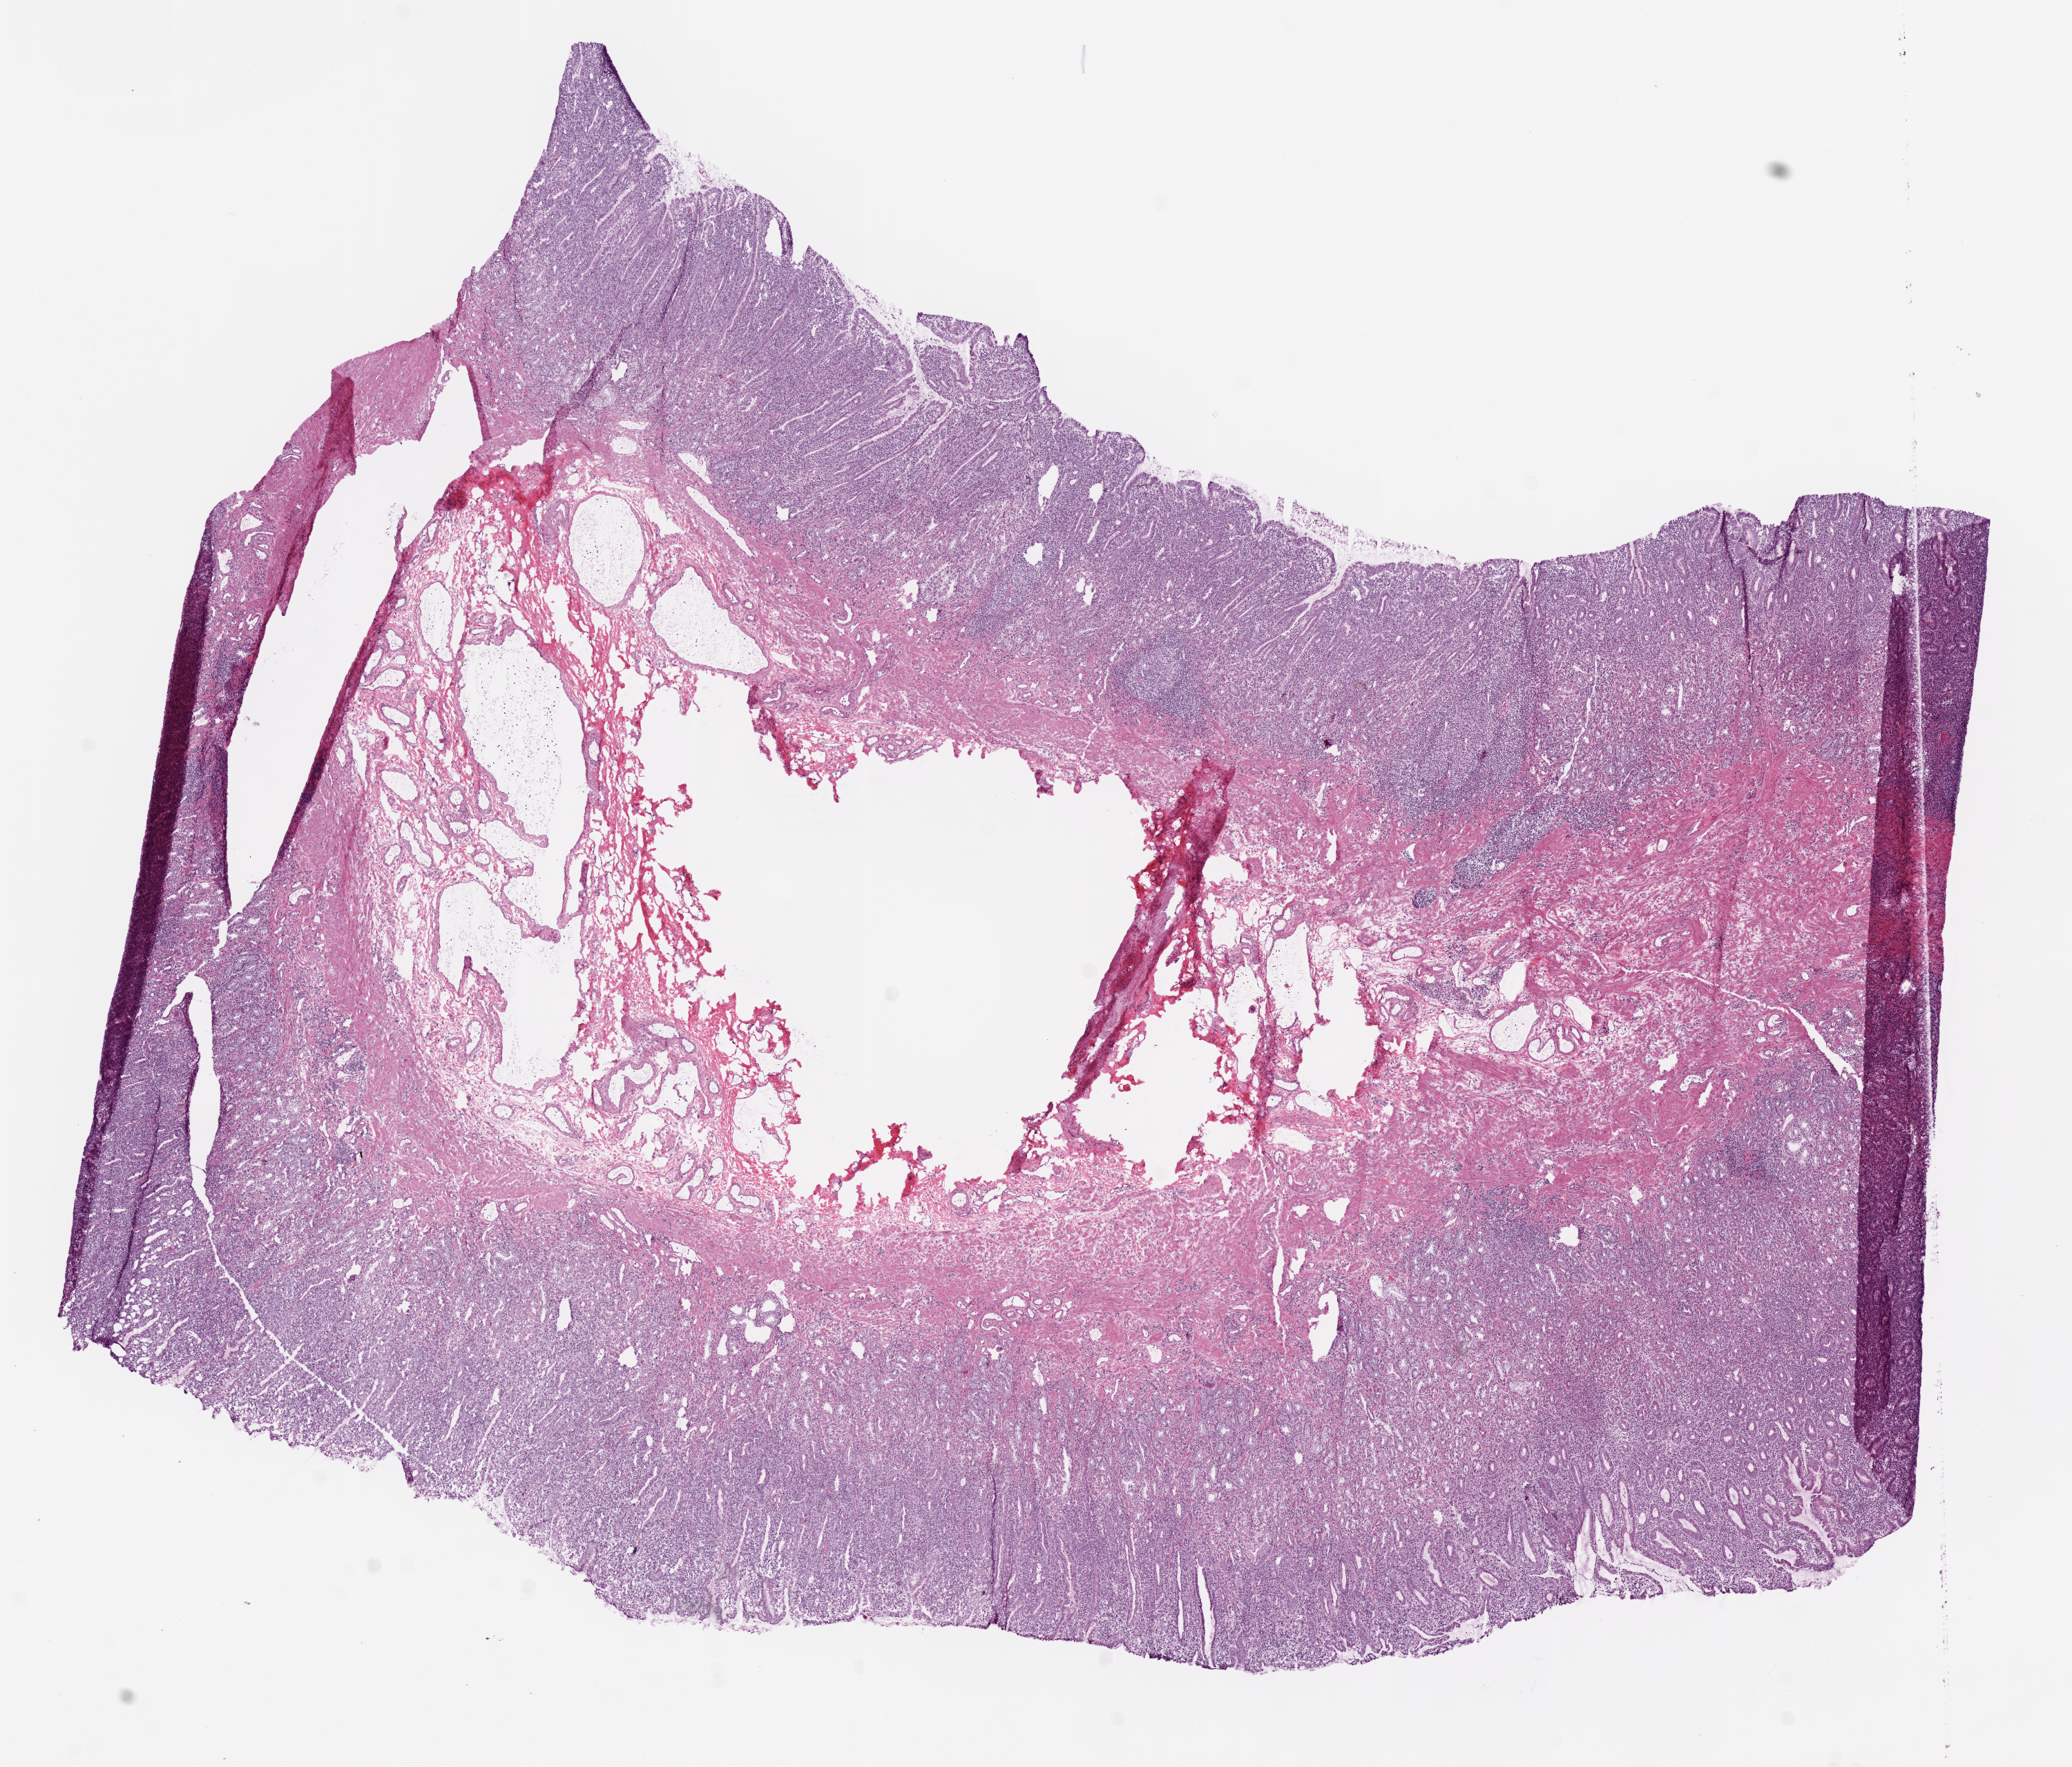
Digitized H&E-stained tissue section (whole slide), whole scanned area (about 12.0 x 10.3 mm, from a 20x scan) shown as a low-resolution overview. Frozen section from the bottom of the tissue portion. Solid tissue normal (non-tumour tissue) sample from the stomach. Female, age 66 years at initial diagnosis.
This section: solid tissue normal sample (biorepository sample class). Patient diagnosis: Adenocarcinoma, NOS (cardia, NOS).